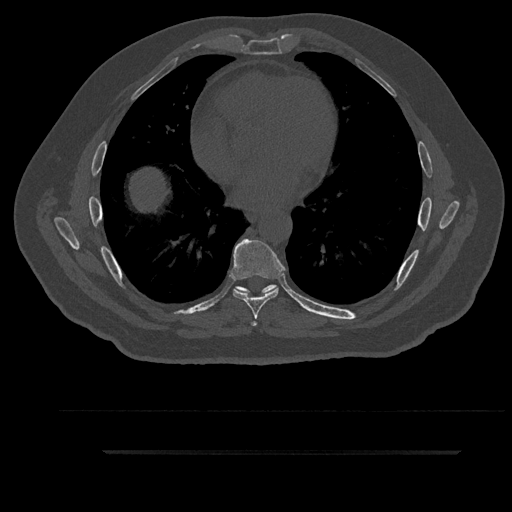
CT including the spine, one axial slice. Slice 513 of 797 in the series (ordered by position). Reconstruction kernel Br40s/3. Bone window (W 1800 / L 400 HU). 0.5 mm slice thickness. 512 × 512 image matrix, field of view 432 × 432 mm. Patient: male, 63 years. From the clinical record (not read from this slice): primary cancer: renal; vertebrae with lytic lesions (as recorded): T8.
Structures marked on this image (semi-automatically segmented with operator editing):
- T6 vertebra: box from (x=235, y=288) to (x=270, y=326) px
- T7 vertebra: (x=232, y=239)–(x=285, y=319)
- T8 vertebra: (x=235, y=284)–(x=278, y=293)